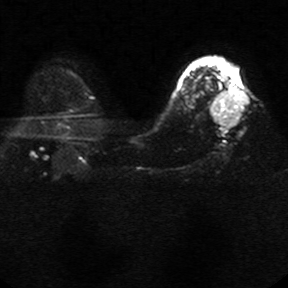
Breast MRI, one axial slice; slice 20 of 34 in the series (ordered by position); diffusion-weighted series; image 2 of 4 stored at this slice position (different b-values; order by instance number); 1.5 T; 5 mm slice thickness; 288 × 288 image matrix, field of view 340 × 340 mm. Female patient.
Outlined on this slice (expert manual segmentation):
- tumour on diffusion-weighted imaging: bounding box (x1, y1, x2, y2) in pixels: (211, 88, 247, 127)